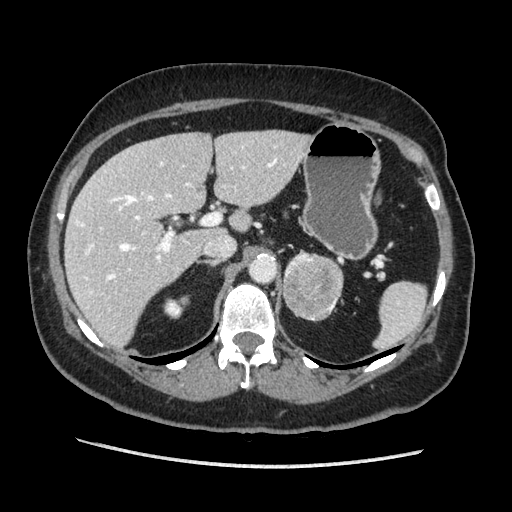
Contrast-enhanced abdominal CT, one axial slice; slice 127 of 203 in the series (ordered by position); soft-tissue window (W 400 / L 40 HU); 1.25 mm slice thickness; 512 × 512 image matrix. Female patient. Case-level facts recorded for this patient, not image findings: diagnosis: adrenocortical carcinoma; tumour side: left adrenal.
Annotated regions visible in this slice (semi-automatic segmentation, software-assisted and operator-edited):
- mass: box from (x=283, y=250) to (x=345, y=321) px